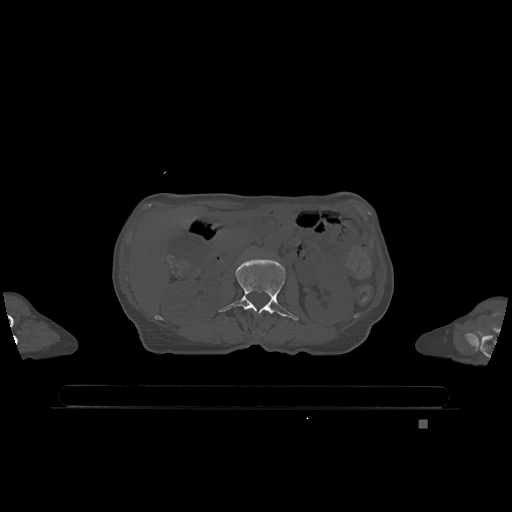
CT including the spine, one axial slice. Slice 416 of 1317 in the series (ordered by position). Bone window (W 1800 / L 400 HU). 0.5 mm slice thickness. 512 × 512 image matrix. Female patient, age 74 years. Case-level facts recorded for this patient, not image findings: primary cancer: lung; vertebrae with lytic lesions (as recorded): T1, T4, T5, T6, L4, L5.
Outlined on this slice (semi-automatic segmentation, software-assisted and operator-edited):
- L2 vertebra: box from (x=218, y=258) to (x=299, y=321) px